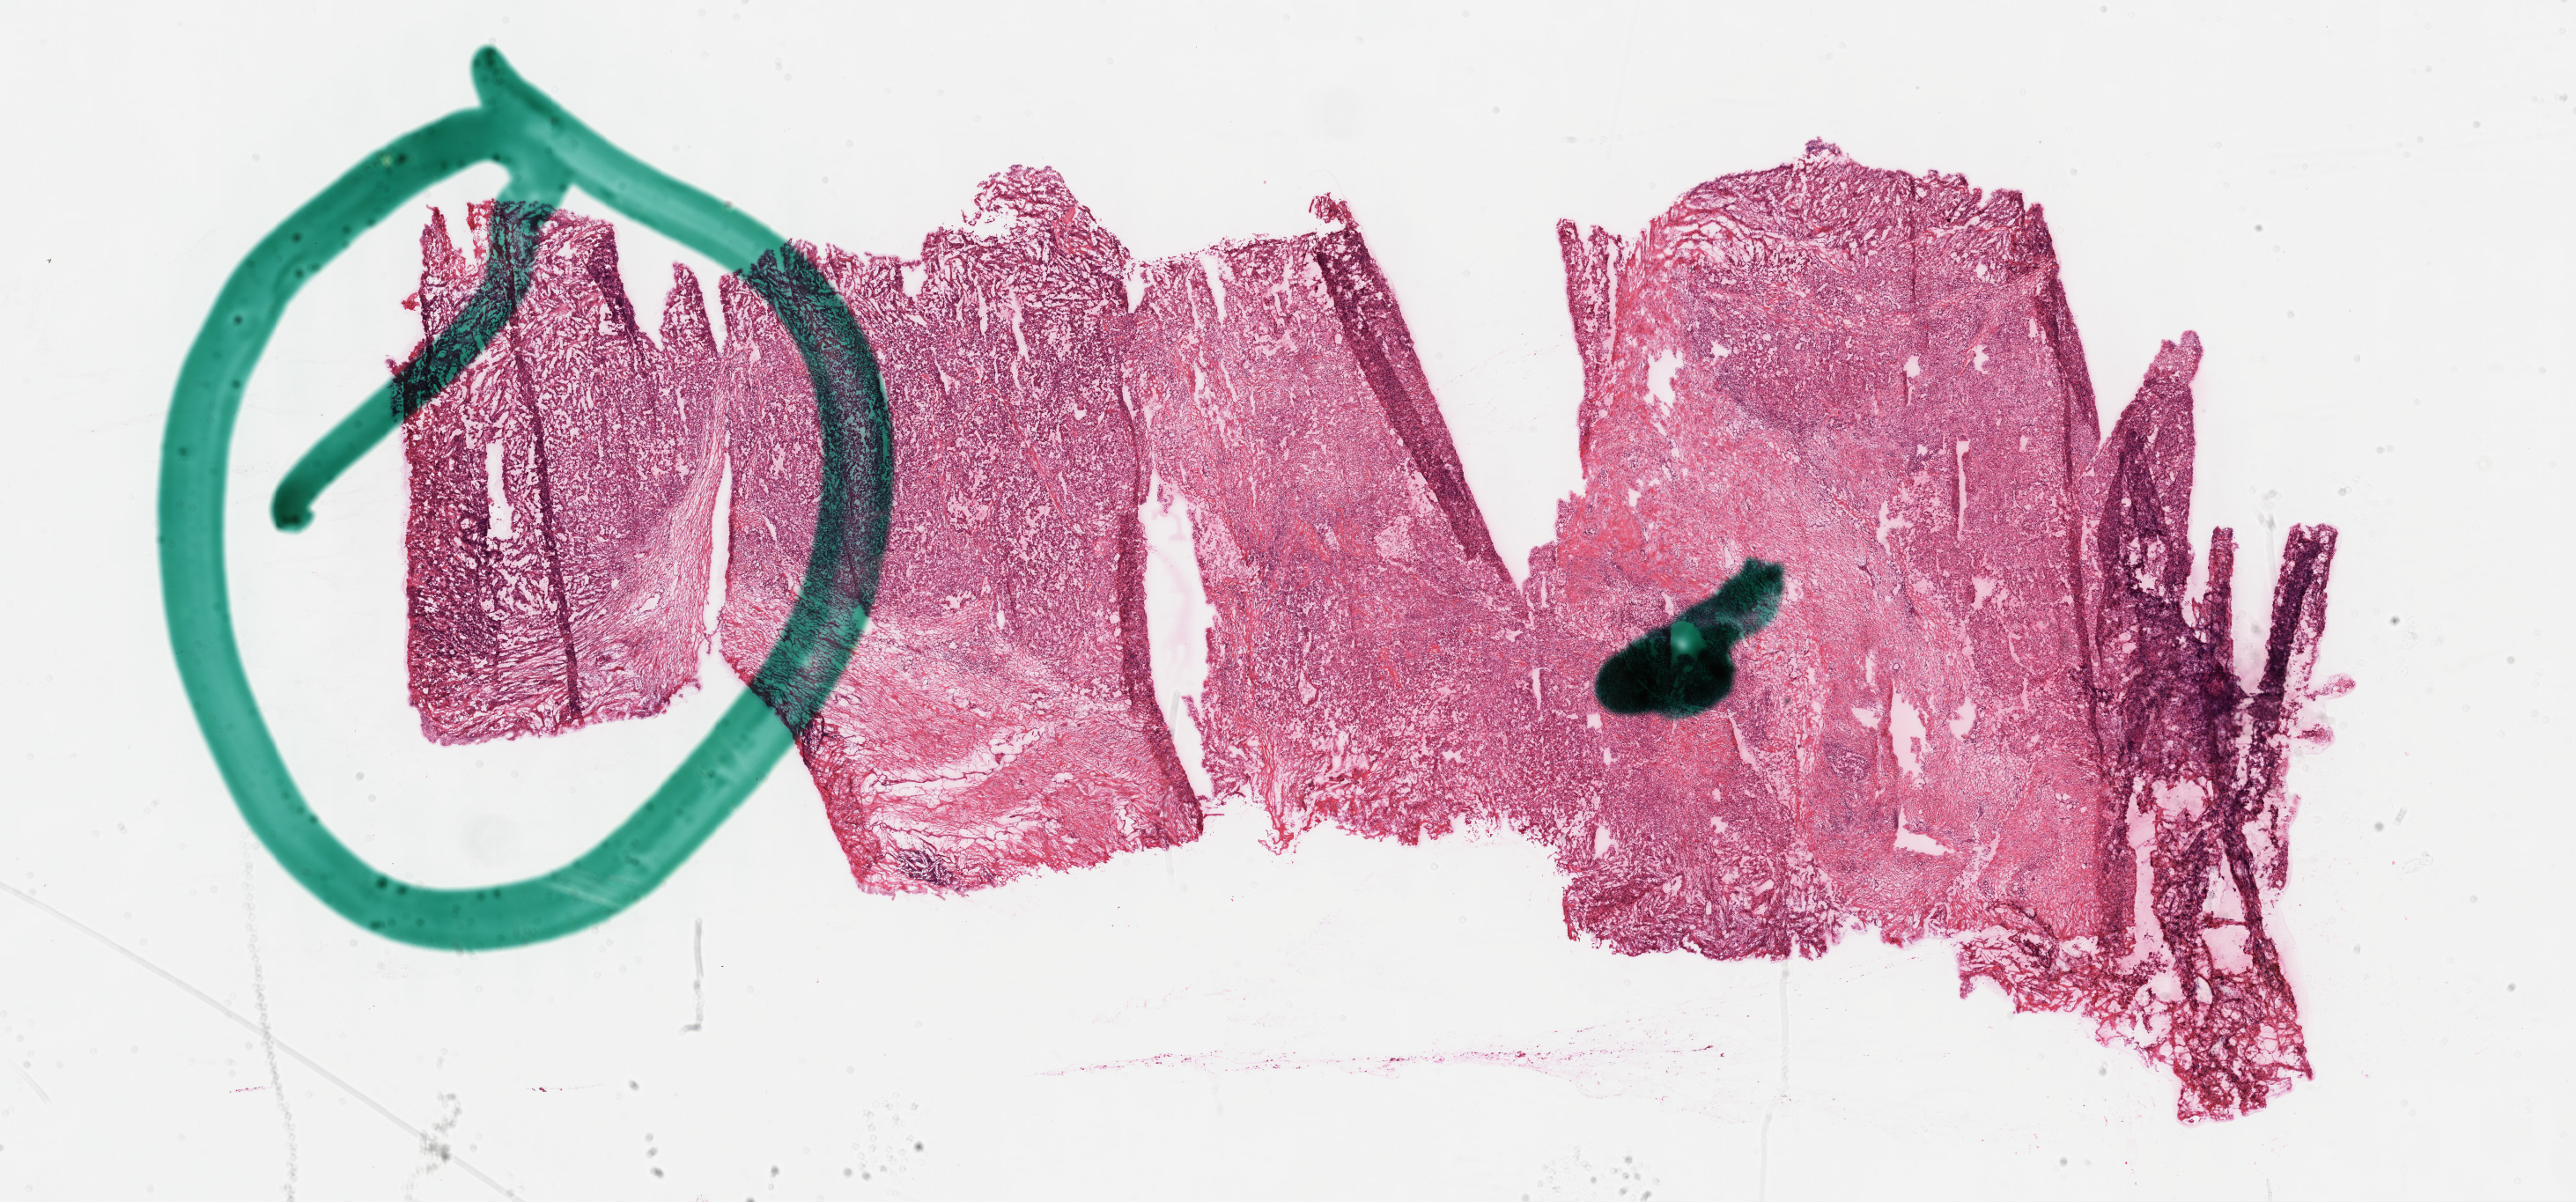
Hematoxylin and eosin (H&E) stained whole-slide image — shown as a low-resolution overview of the whole scanned area (about 23.7 x 11.0 mm, slide scanned at 40x), formalin-fixed paraffin-embedded (FFPE) diagnostic section, primary tumour sample from the kidney. Patient: female, age at initial diagnosis 54 years.
Diagnosis: Clear cell adenocarcinoma, NOS.